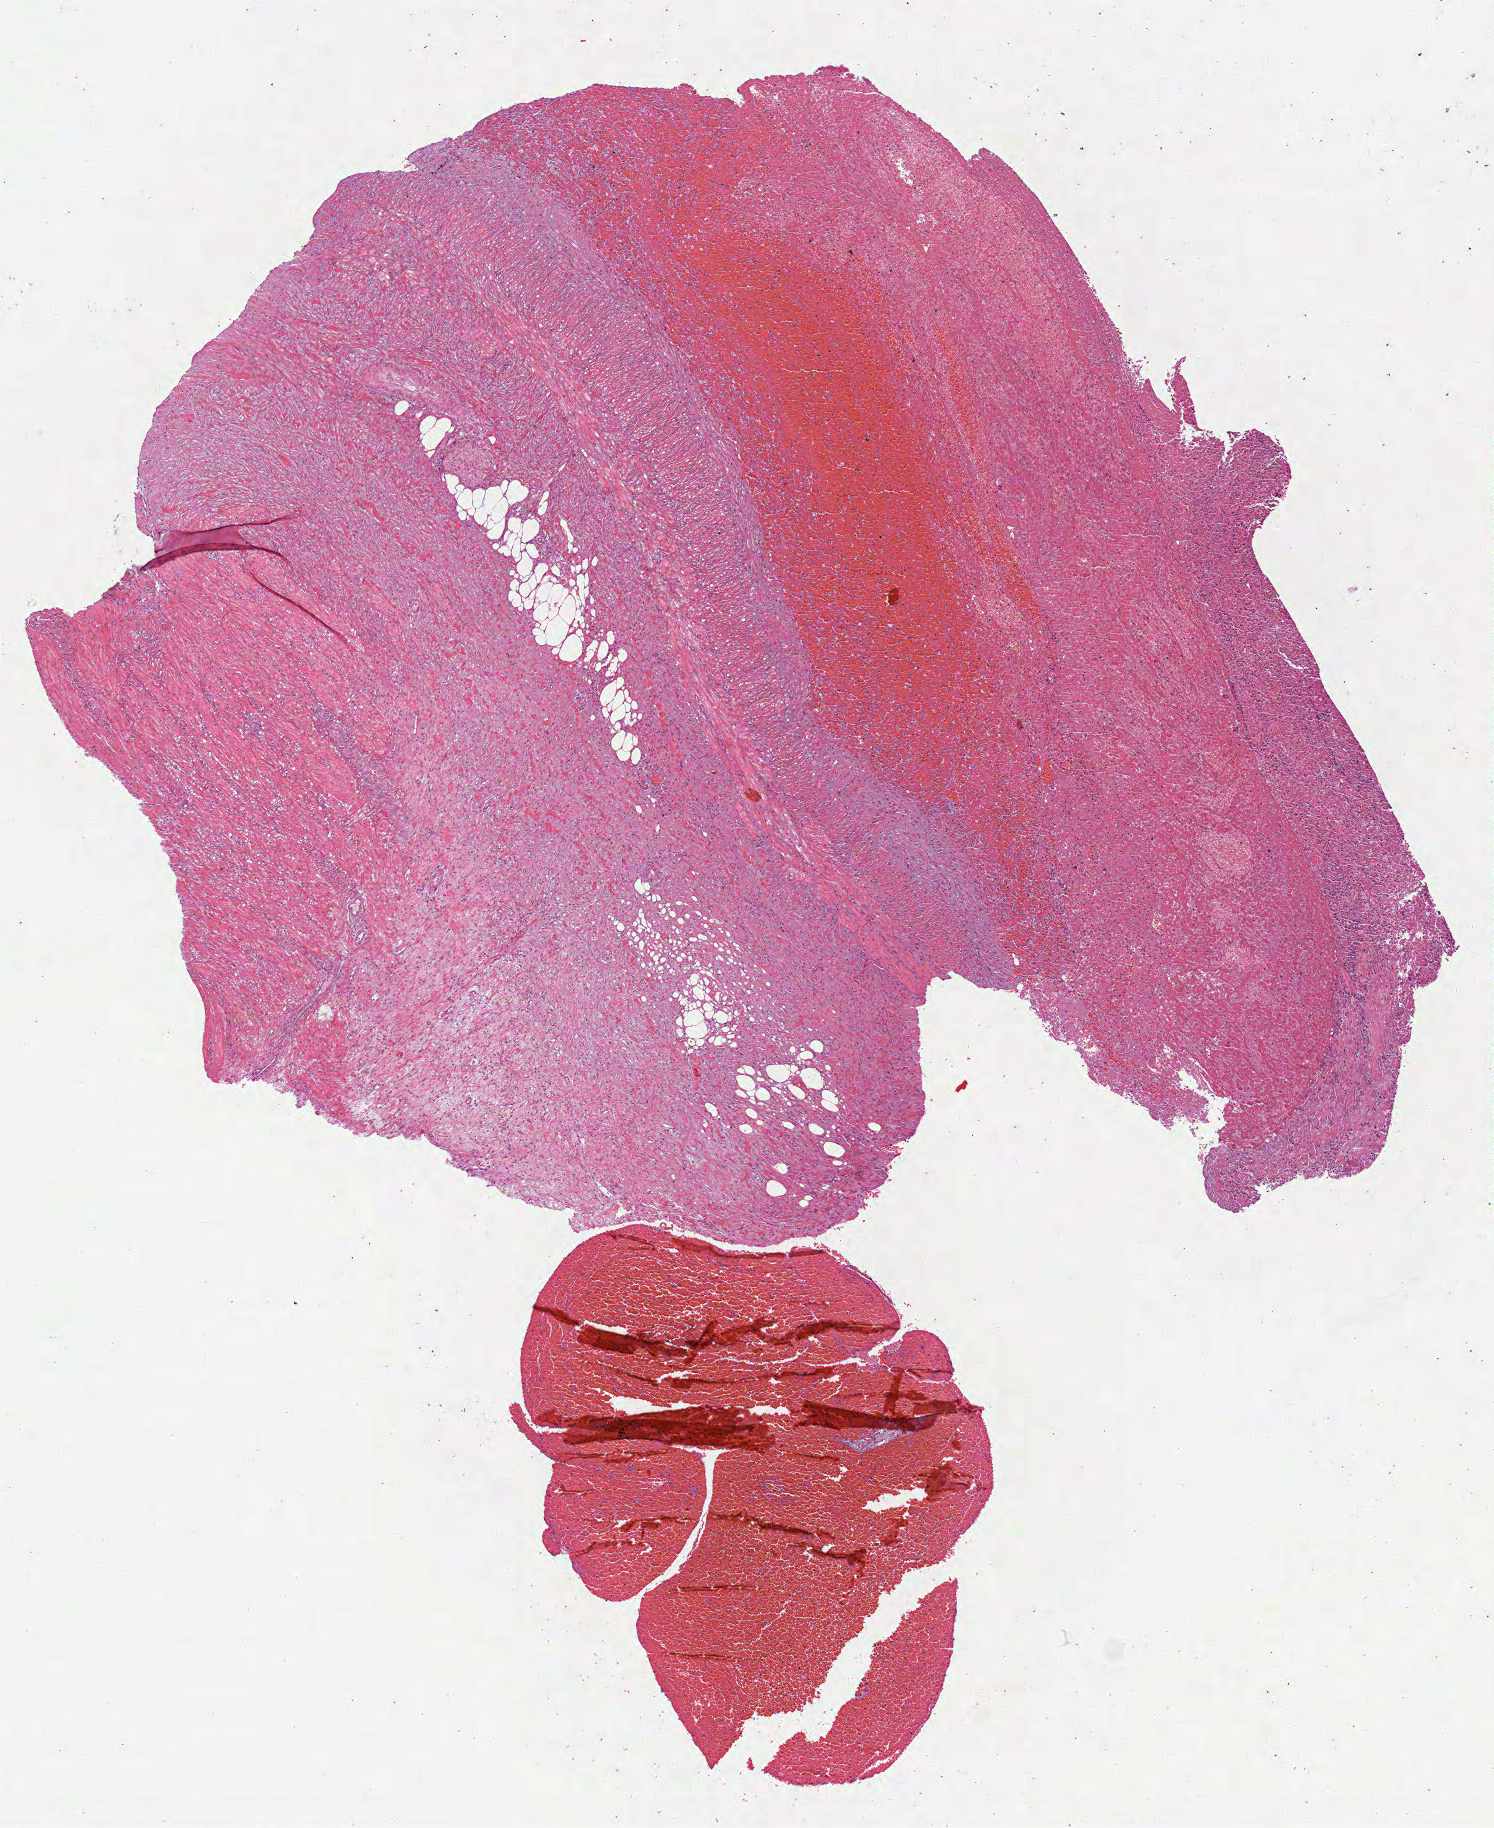
H&E whole-slide image — shown as a low-resolution overview of the whole scanned area (about 6.0 x 7.4 mm, from a 40x scan), FFPE section, sample: primary tumour, uterus. Patient: female, age at initial diagnosis 56 years.
* pathologic diagnosis: Leiomyosarcoma, NOS